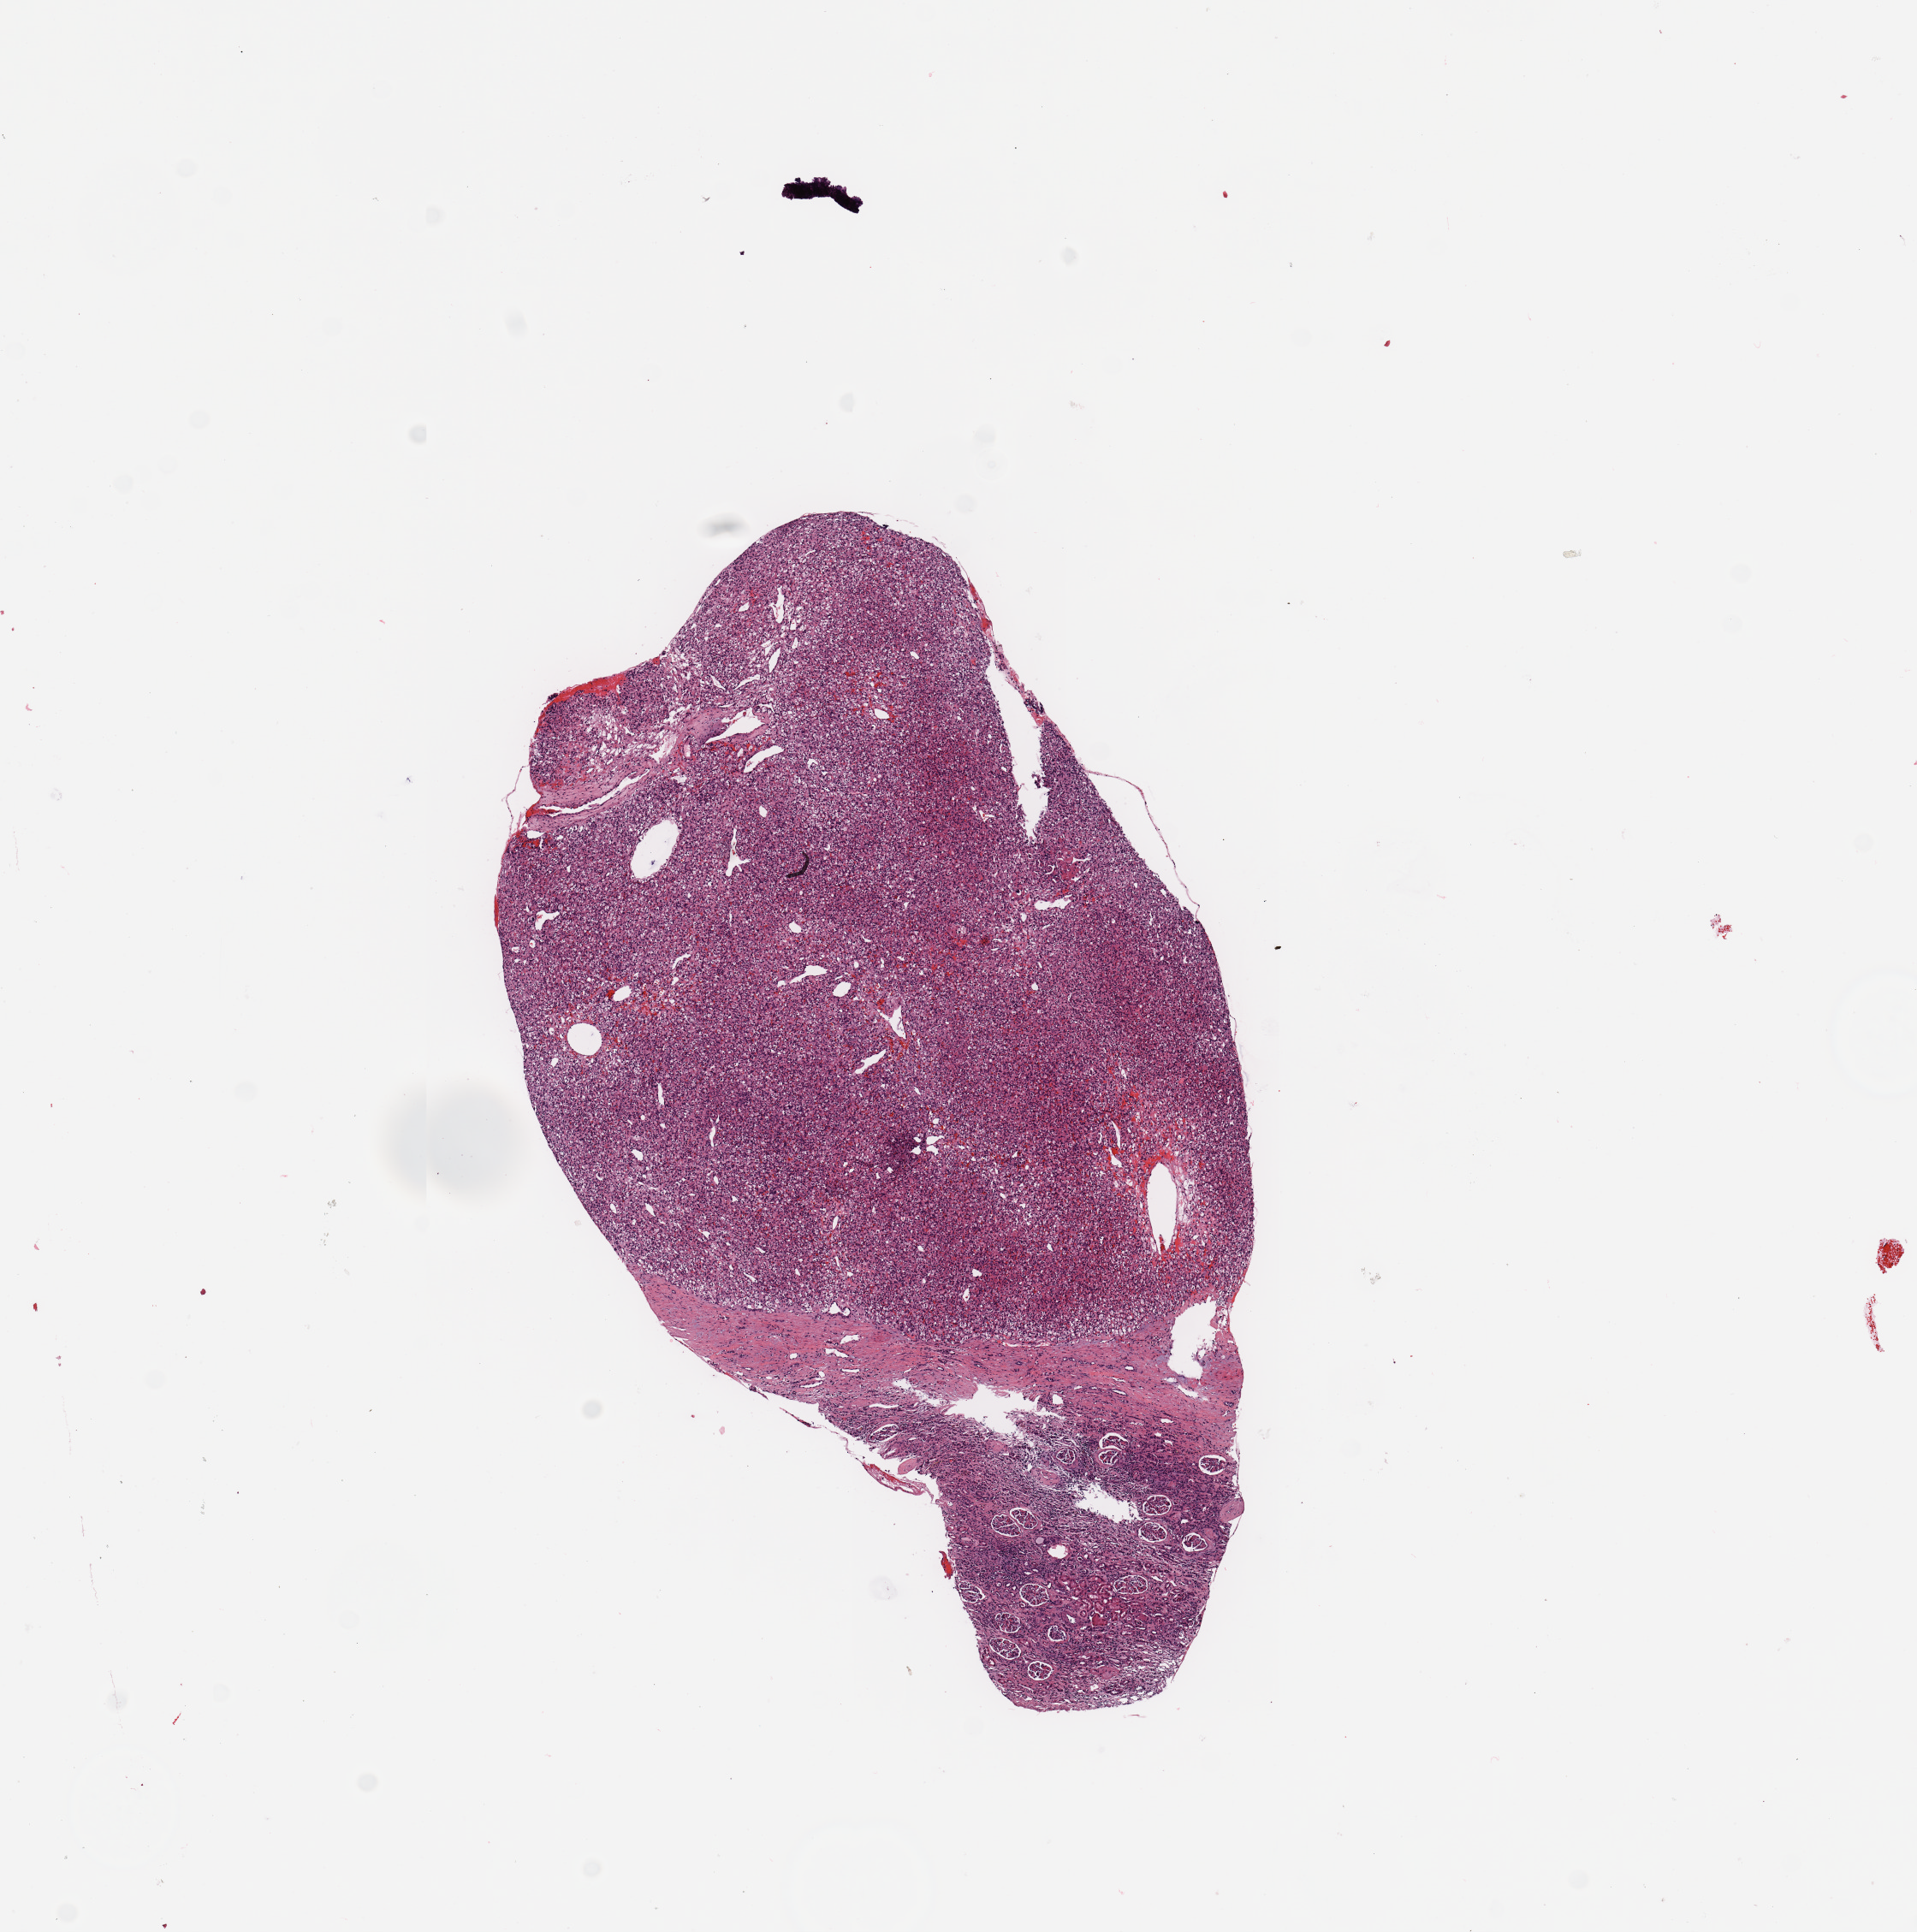
Digitized H&E-stained tissue section (whole slide) — low-resolution overview of the scanned area, about 8.9 x 8.9 mm, tumour tissue sample, sampled site: kidney. 57-year-old female patient. Slide review estimates, as recorded: tumour nuclei 85%, necrosis 0%.
Histologic diagnosis: Renal cell carcinoma, NOS.